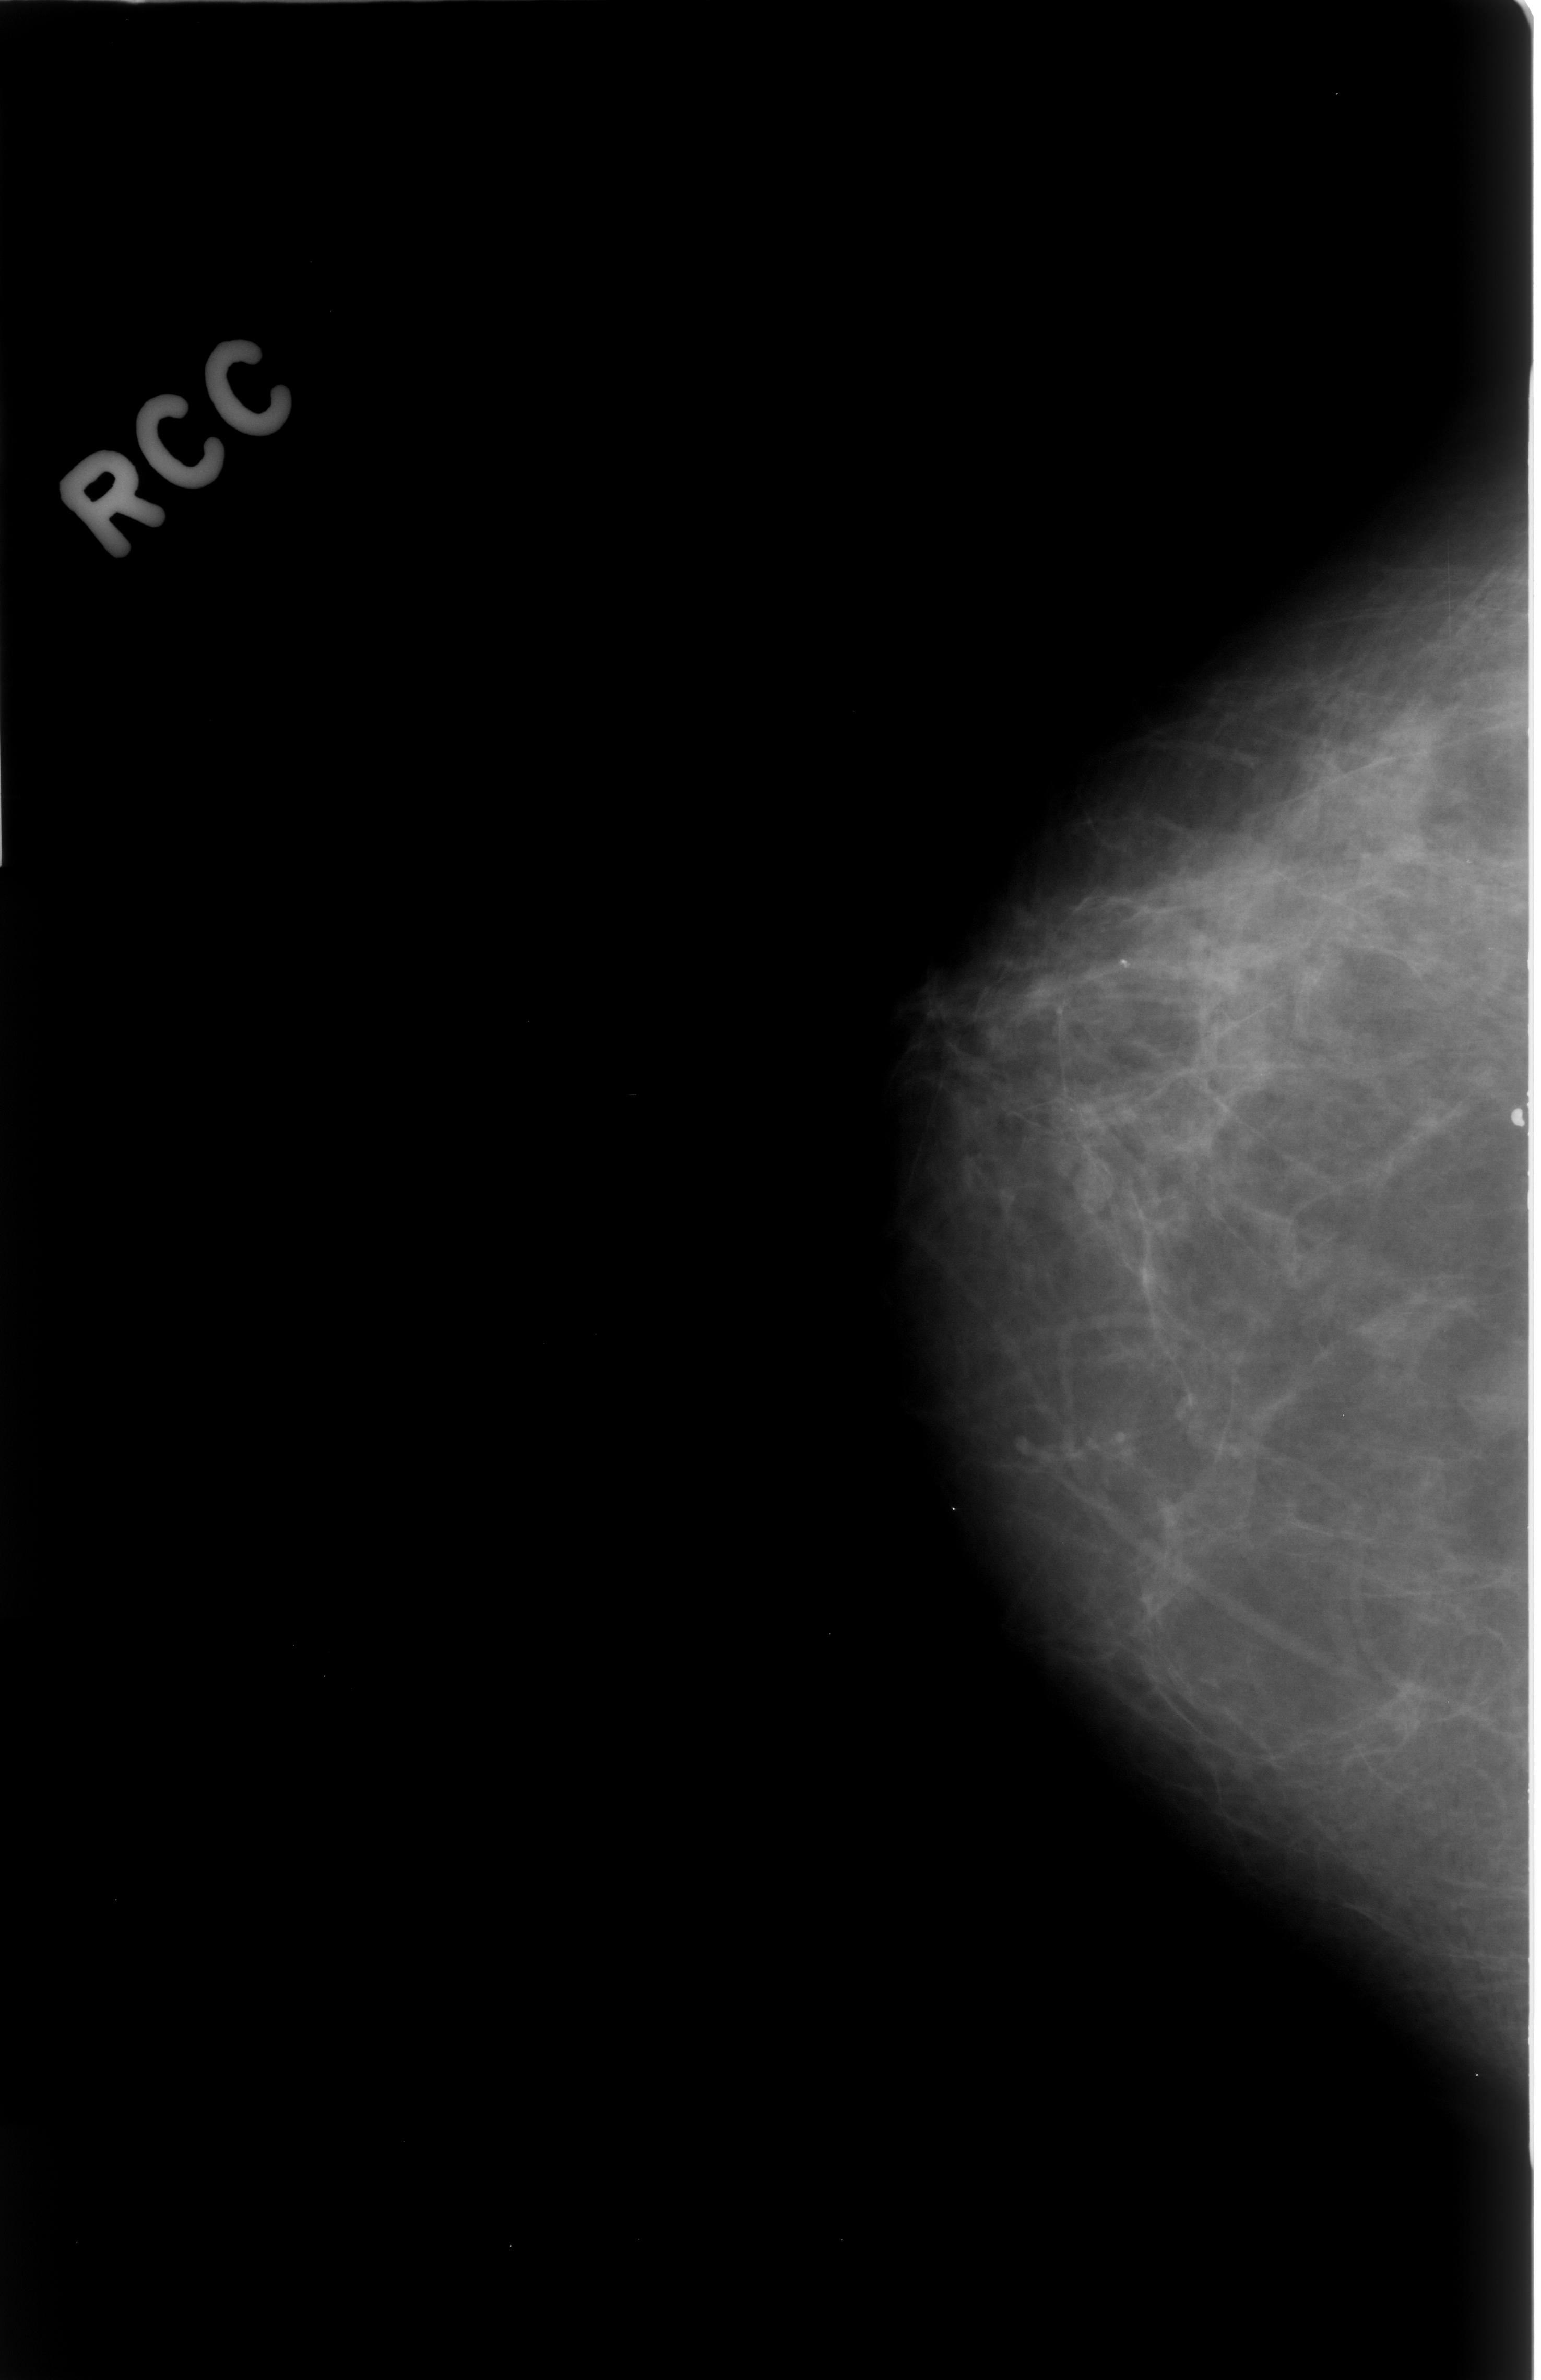
Digitized screen-film mammogram, right breast, craniocaudal (CC) view.
Marked findings (only marked abnormalities are described; nothing is implied about the rest of the image): mass, shape round, margins circumscribed; BI-RADS assessment category 3; subtlety rating 3 on a 1 (subtle) to 5 (obvious) scale; benign; no additional work-up was recommended (benign without callback).